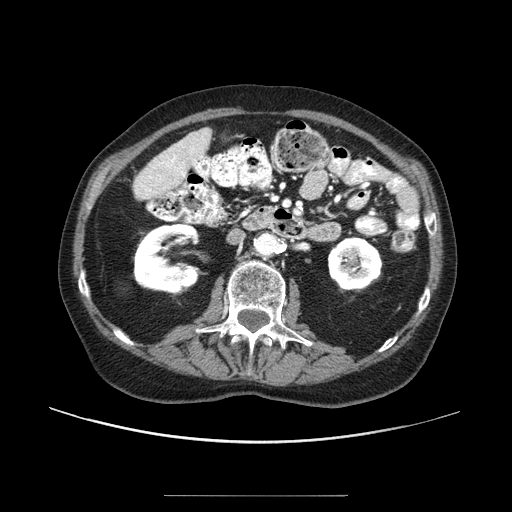
Contrast-enhanced abdominal CT (liver protocol), one axial slice; position 29 of 91 along the scan axis; 100 kVp; one of 2 acquisitions stored at this slice position; soft-tissue window (W 400 / L 40 HU); 512 × 512 image matrix. From the clinical record (not read from this slice): diagnosis: hepatocellular carcinoma (patient treated with transarterial chemoembolisation; whether this scan precedes or follows treatment is not stated here); TNM stage (as recorded): Stage-I; Child-Pugh class: A.
Outlined on this slice (semi-automatic segmentation, software-assisted and operator-edited):
- liver parenchyma outside the tumour (the mass and vessels are separate outlines, so this box may not span the whole liver): box from (x=148, y=128) to (x=212, y=186) px
- liver vessels: (x=154, y=142)–(x=202, y=176)